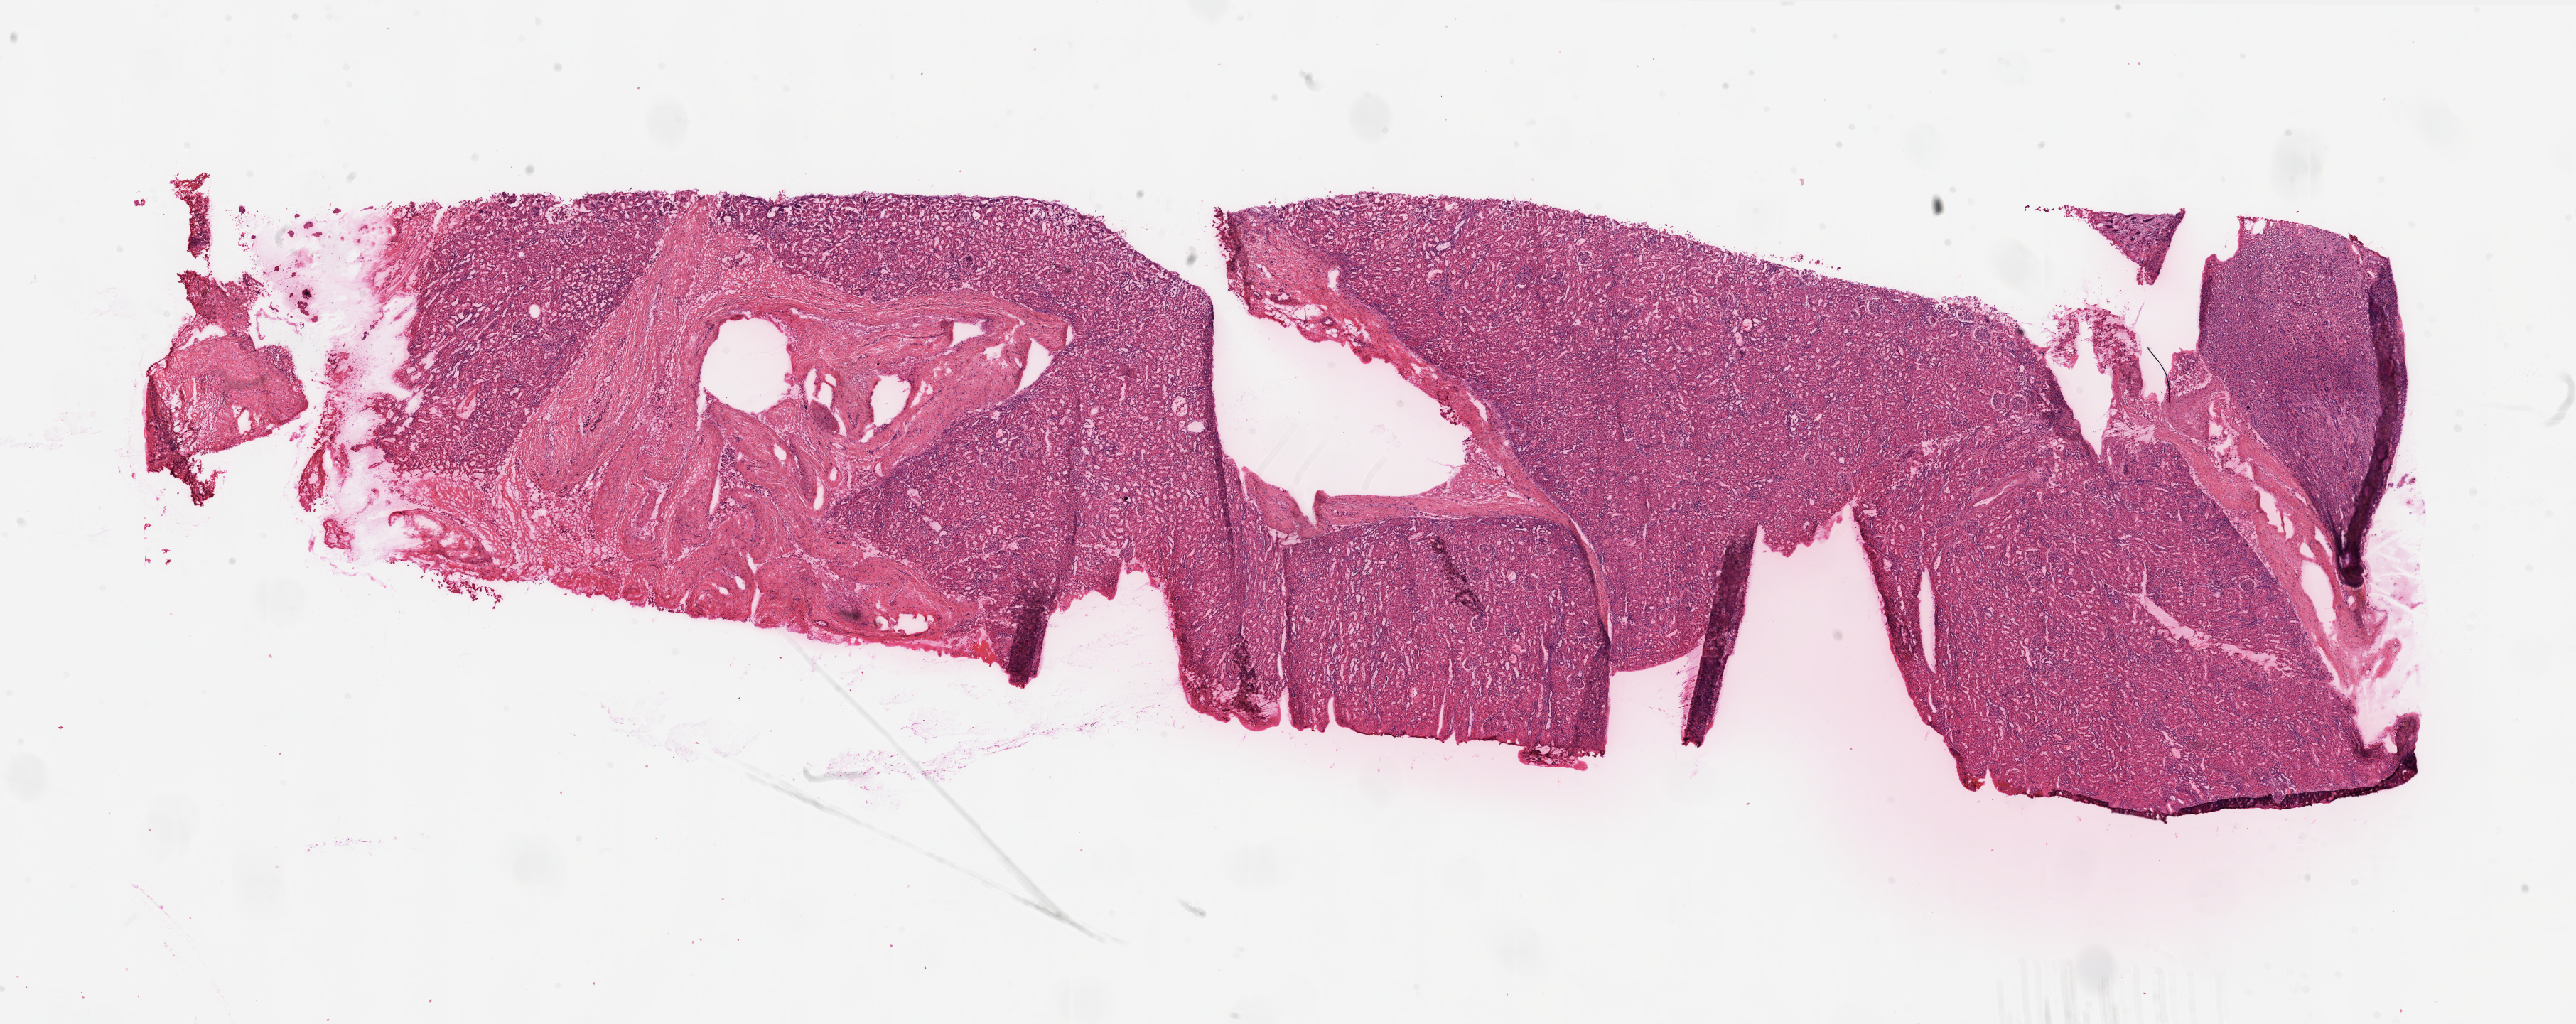
Whole-slide histology image, Hematoxylin and eosin (H&E) stained, low-resolution overview of the scanned area, about 29.1 x 11.6 mm (slide scanned at 20x); frozen section from the top of the tissue portion; kidney, solid tissue normal (non-tumour tissue) sample. Female, age 42 years at initial diagnosis.
This section: solid tissue normal (non-tumour) sample from the same patient. Patient diagnosis: Clear cell adenocarcinoma, NOS.